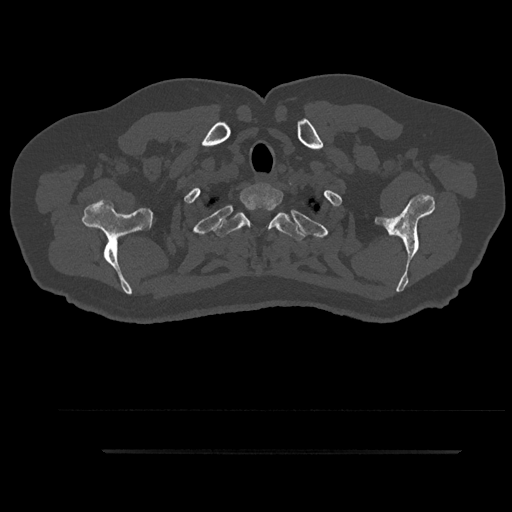
CT including the spine, one axial slice; slice 775 of 797 in the series (ordered by position); 120 kVp; bone window (W 1800 / L 400 HU); 512 × 512 image matrix, field of view 432 × 432 mm. Patient: male, 63 years. Case-level facts recorded for this patient, not image findings: primary cancer: renal; vertebrae with lytic lesions (as recorded): T8.
Outlined on this slice (semi-automatic segmentation, software-assisted and operator-edited):
- T1 vertebra: box from (x=239, y=185) to (x=283, y=211) px
- T2 vertebra: (x=213, y=209)–(x=306, y=240)